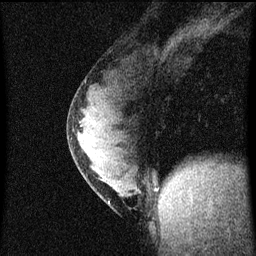
Breast MRI (dynamic contrast-enhanced), one sagittal slice; position 28 of 60 along the scan axis; dynamic contrast-enhanced series, image 2 of 4 at this slice position (ordered by acquisition); 1.5 T; TE 4.2 ms, TR 8 ms; 2 mm slice thickness; 256 × 256 image matrix, field of view 180 × 180 mm. Female patient, age 33 years.
Annotated regions visible in this slice (semi-automatic segmentation, software-assisted and operator-edited):
- analysis volume of interest (the breast-tissue region the enhancement analysis was run in; not a lesion): bounding box (x1, y1, x2, y2) in pixels: (68, 76, 150, 215)
- tumour enhancement mask (voxels above the 70 % enhancement threshold inside the analysis volume of interest): (77, 134, 110, 205)